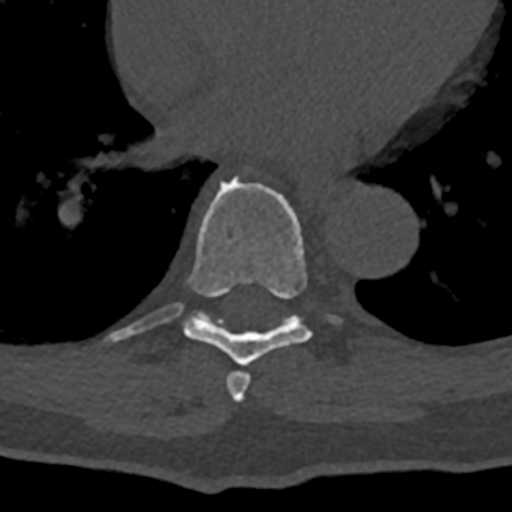
CT including the spine, one axial slice. Position 704 of 797 along the scan axis. Reconstruction kernel Br40s/3. 120 kVp. Bone window (W 1800 / L 400 HU). 0.5 mm slice thickness. 512 × 512 image matrix, field of view 160 × 160 mm. Male patient, age 74 years. Case-level facts recorded for this patient, not image findings: primary cancer: renal; vertebrae with lytic lesions (as recorded): T10, L1, L2, L3, L4, L5.
Annotated regions visible in this slice (semi-automatically segmented with operator editing):
- T7 vertebra: bounding box [x1, y1, x2, y2] px = [226, 371, 251, 402]
- T8 vertebra: [104, 176, 342, 366]